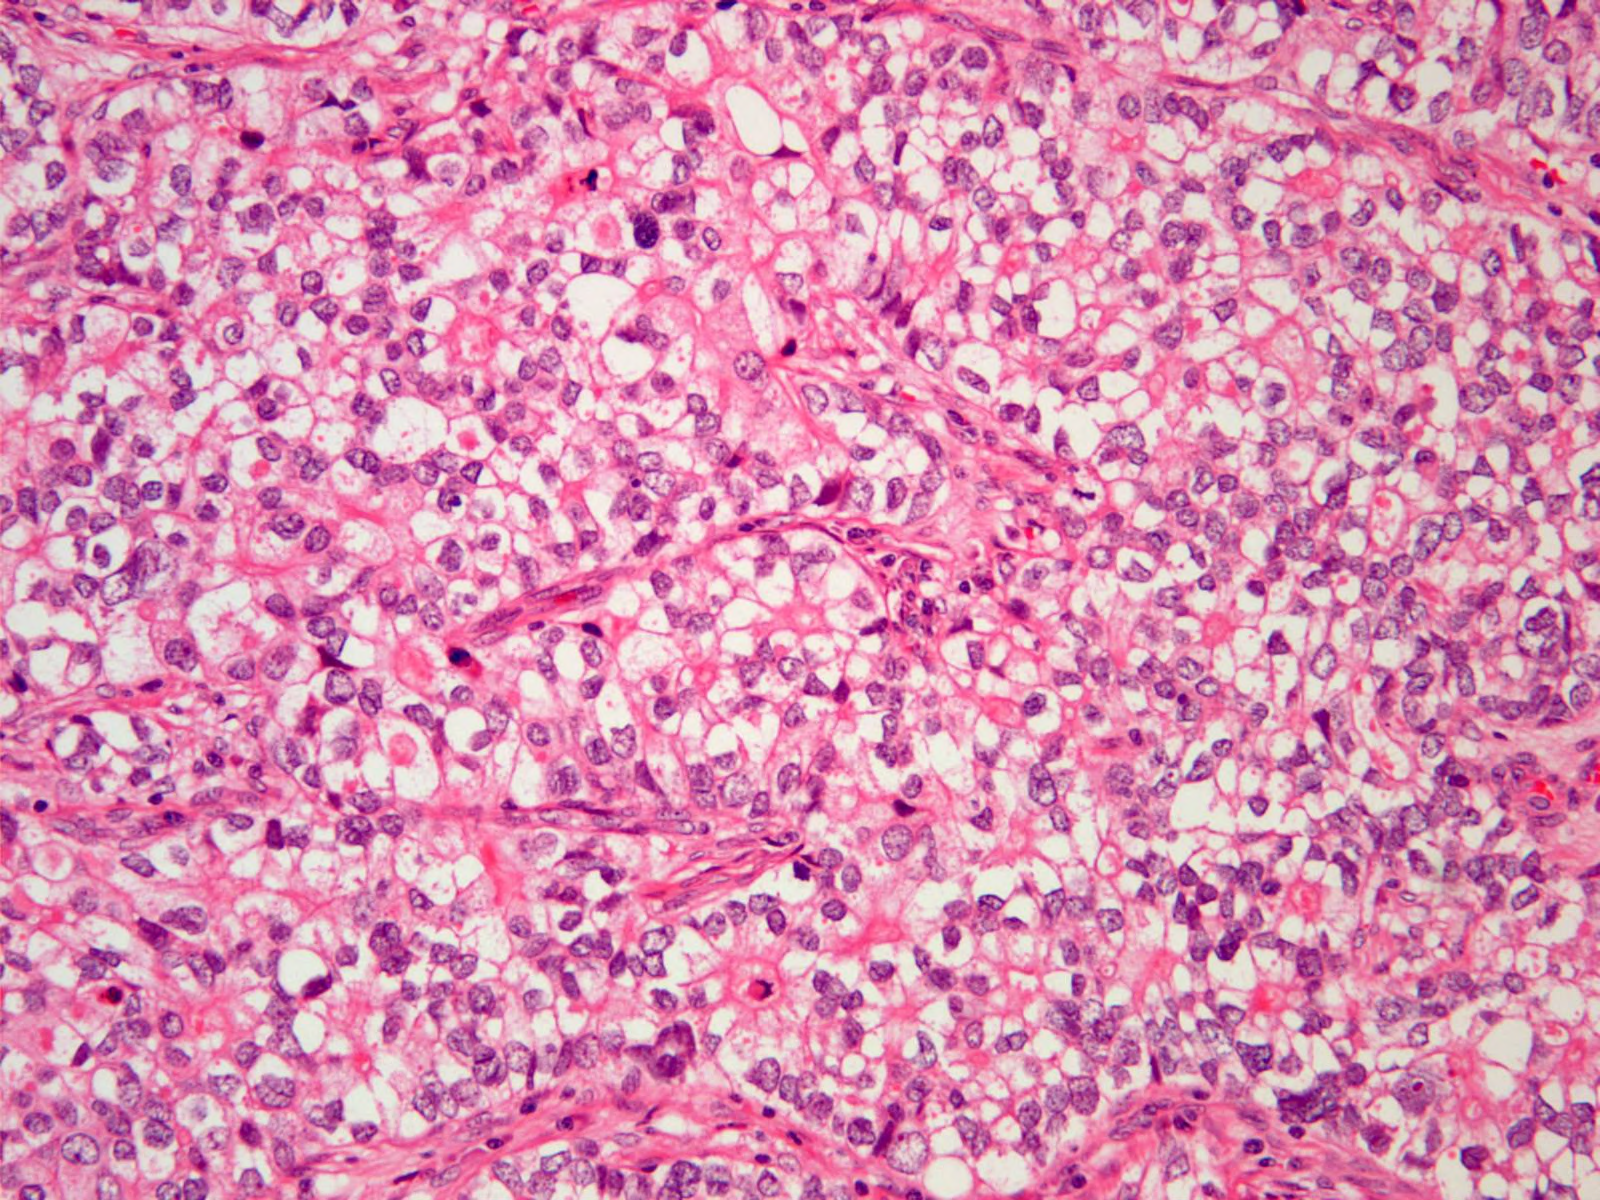
H&E image of one small field of the section — covering about 0.8 x 0.6 mm. Formalin-fixed paraffin-embedded (FFPE) diagnostic section. Sample: primary tumour, stomach. Male patient; age at initial diagnosis 75 years. Histologic grade: G3 (poorly differentiated).
* pathologic diagnosis: Adenocarcinoma, NOS (cardia, NOS)